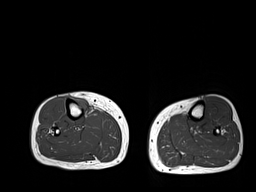
MRI of an extremity soft-tissue mass, one axial slice. Slice 12 of 32 in the series (ordered by position). 6 mm slice thickness. 256 × 192 image matrix, field of view 375 × 281 mm. Female patient. From the clinical record (not read from this slice): histological type: undifferentiated – high grade; grade: high; site of the primary tumour: right thigh.
Structures marked on this image (manually delineated by an expert):
- gross tumour volume (mass): box from (x=74, y=96) to (x=90, y=114) px